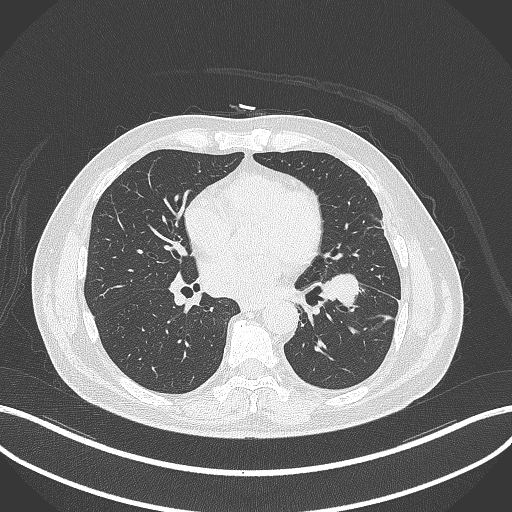
Chest CT, one axial slice; slice 166 of 230 in the series (ordered by position); reconstruction kernel B70f; 120 kVp; lung window (W 1500 / L -600 HU); 1 mm slice thickness; 512 × 512 image matrix, field of view 400 × 400 mm. Patient: male, 68 years. From the clinical record (not read from this slice): clinical TNM (as recorded): T2b N0 M0.
Structures marked on this image (bounding box drawn by a radiologist):
- lung tumour (recorded histology: squamous cell carcinoma): bounding box [x1, y1, x2, y2] px = [318, 268, 365, 313]